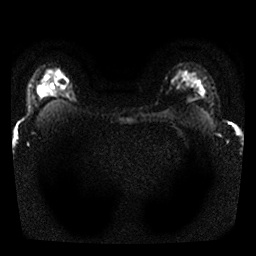
Breast MRI, one axial slice; slice 22 of 25 in the series (ordered by position); diffusion-weighted series; image 2 of 4 stored at this slice position (different b-values; order by instance number); 1.5 T; 4 mm slice thickness; 256 × 256 image matrix. Female patient.
Outlined on this slice (manually delineated by an expert):
- tumour on diffusion-weighted imaging: bounding box <54,70,64,88> (left, top, right, bottom; pixels)